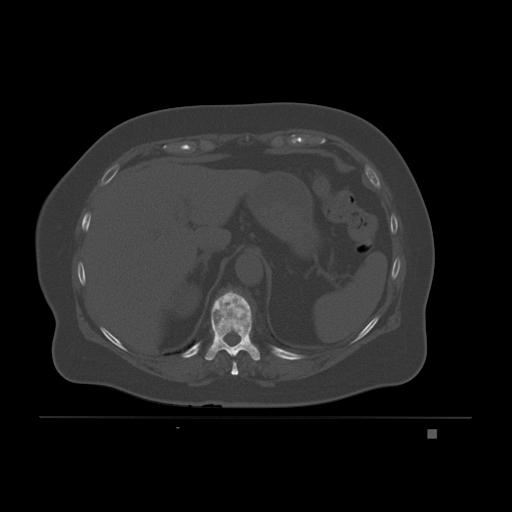
CT including the spine, one axial slice. Position 100 of 221 along the scan axis. Bone window (W 1800 / L 400 HU). 3 mm slice thickness. 512 × 512 image matrix, field of view 474 × 474 mm. Patient: female, 63 years. From the clinical record (not read from this slice): primary cancer: breast.
Annotated regions visible in this slice (semi-automatic segmentation, software-assisted and operator-edited):
- T10 vertebra: bounding box <204,290,261,361> (left, top, right, bottom; pixels)
- T9 vertebra: <231,361,239,376>